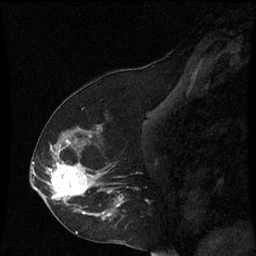
Breast MRI (dynamic contrast-enhanced), one sagittal slice; slice 36 of 60 in the series (ordered by position); dynamic contrast-enhanced series, image 2 of 3 at this slice position (ordered by acquisition); 1.5 T; TE 4.2 ms, TR 8.9 ms; 2 mm slice thickness; 256 × 256 image matrix, field of view 200 × 200 mm. Female patient, age 53 years. From the clinical record (not read from this slice): setting: breast cancer imaged before/during neoadjuvant chemotherapy; receptor status: HR-positive, HER2-negative.
Structures marked on this image (semi-automatic segmentation, software-assisted and operator-edited):
- analysis volume of interest (the breast-tissue region the enhancement analysis was run in; not a lesion): bounding box (x1, y1, x2, y2) in pixels: (38, 128, 125, 229)
- tumour enhancement mask (voxels above the 70 % enhancement threshold inside the analysis volume of interest): (48, 140, 123, 219)